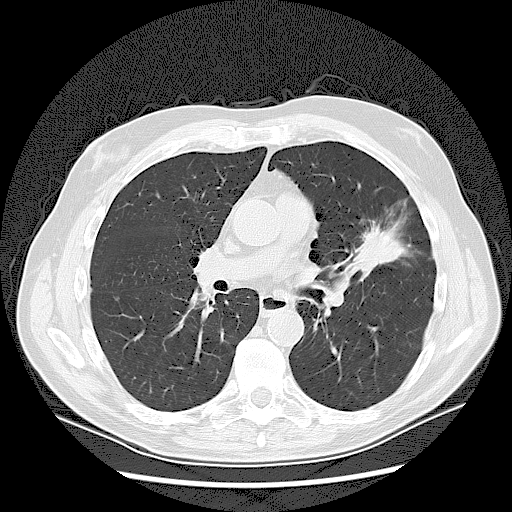
Chest CT (low-dose screening protocol), one axial image, baseline screening round, lung window (W 1500 / L -600 HU), 2.5 mm slice thickness, slice 61 of 132 in the series, 512 × 512 image matrix, field of view 380 × 380 mm. Male, age 65 years at enrolment.
Expert reader's lesion annotation, bounding box <348,221,399,267> (left, top, right, bottom; pixels). Reader record for this screening exam (exam-level; its link to the box is not recorded): non-calcified nodule or mass ≥4 mm, left upper lobe, 37 × 27 mm, spiculated (stellate) margins, soft tissue attenuation. Official screen result: positive, change unspecified: nodule(s) >= 4 mm or enlarging nodule(s), mass(es), or other non-specific abnormalities suspicious for lung cancer. Participant outcome: lung cancer diagnosed 56 days after this screen — non-small cell carcinoma, poorly differentiated (G3), stage IA (AJCC 6th edition).